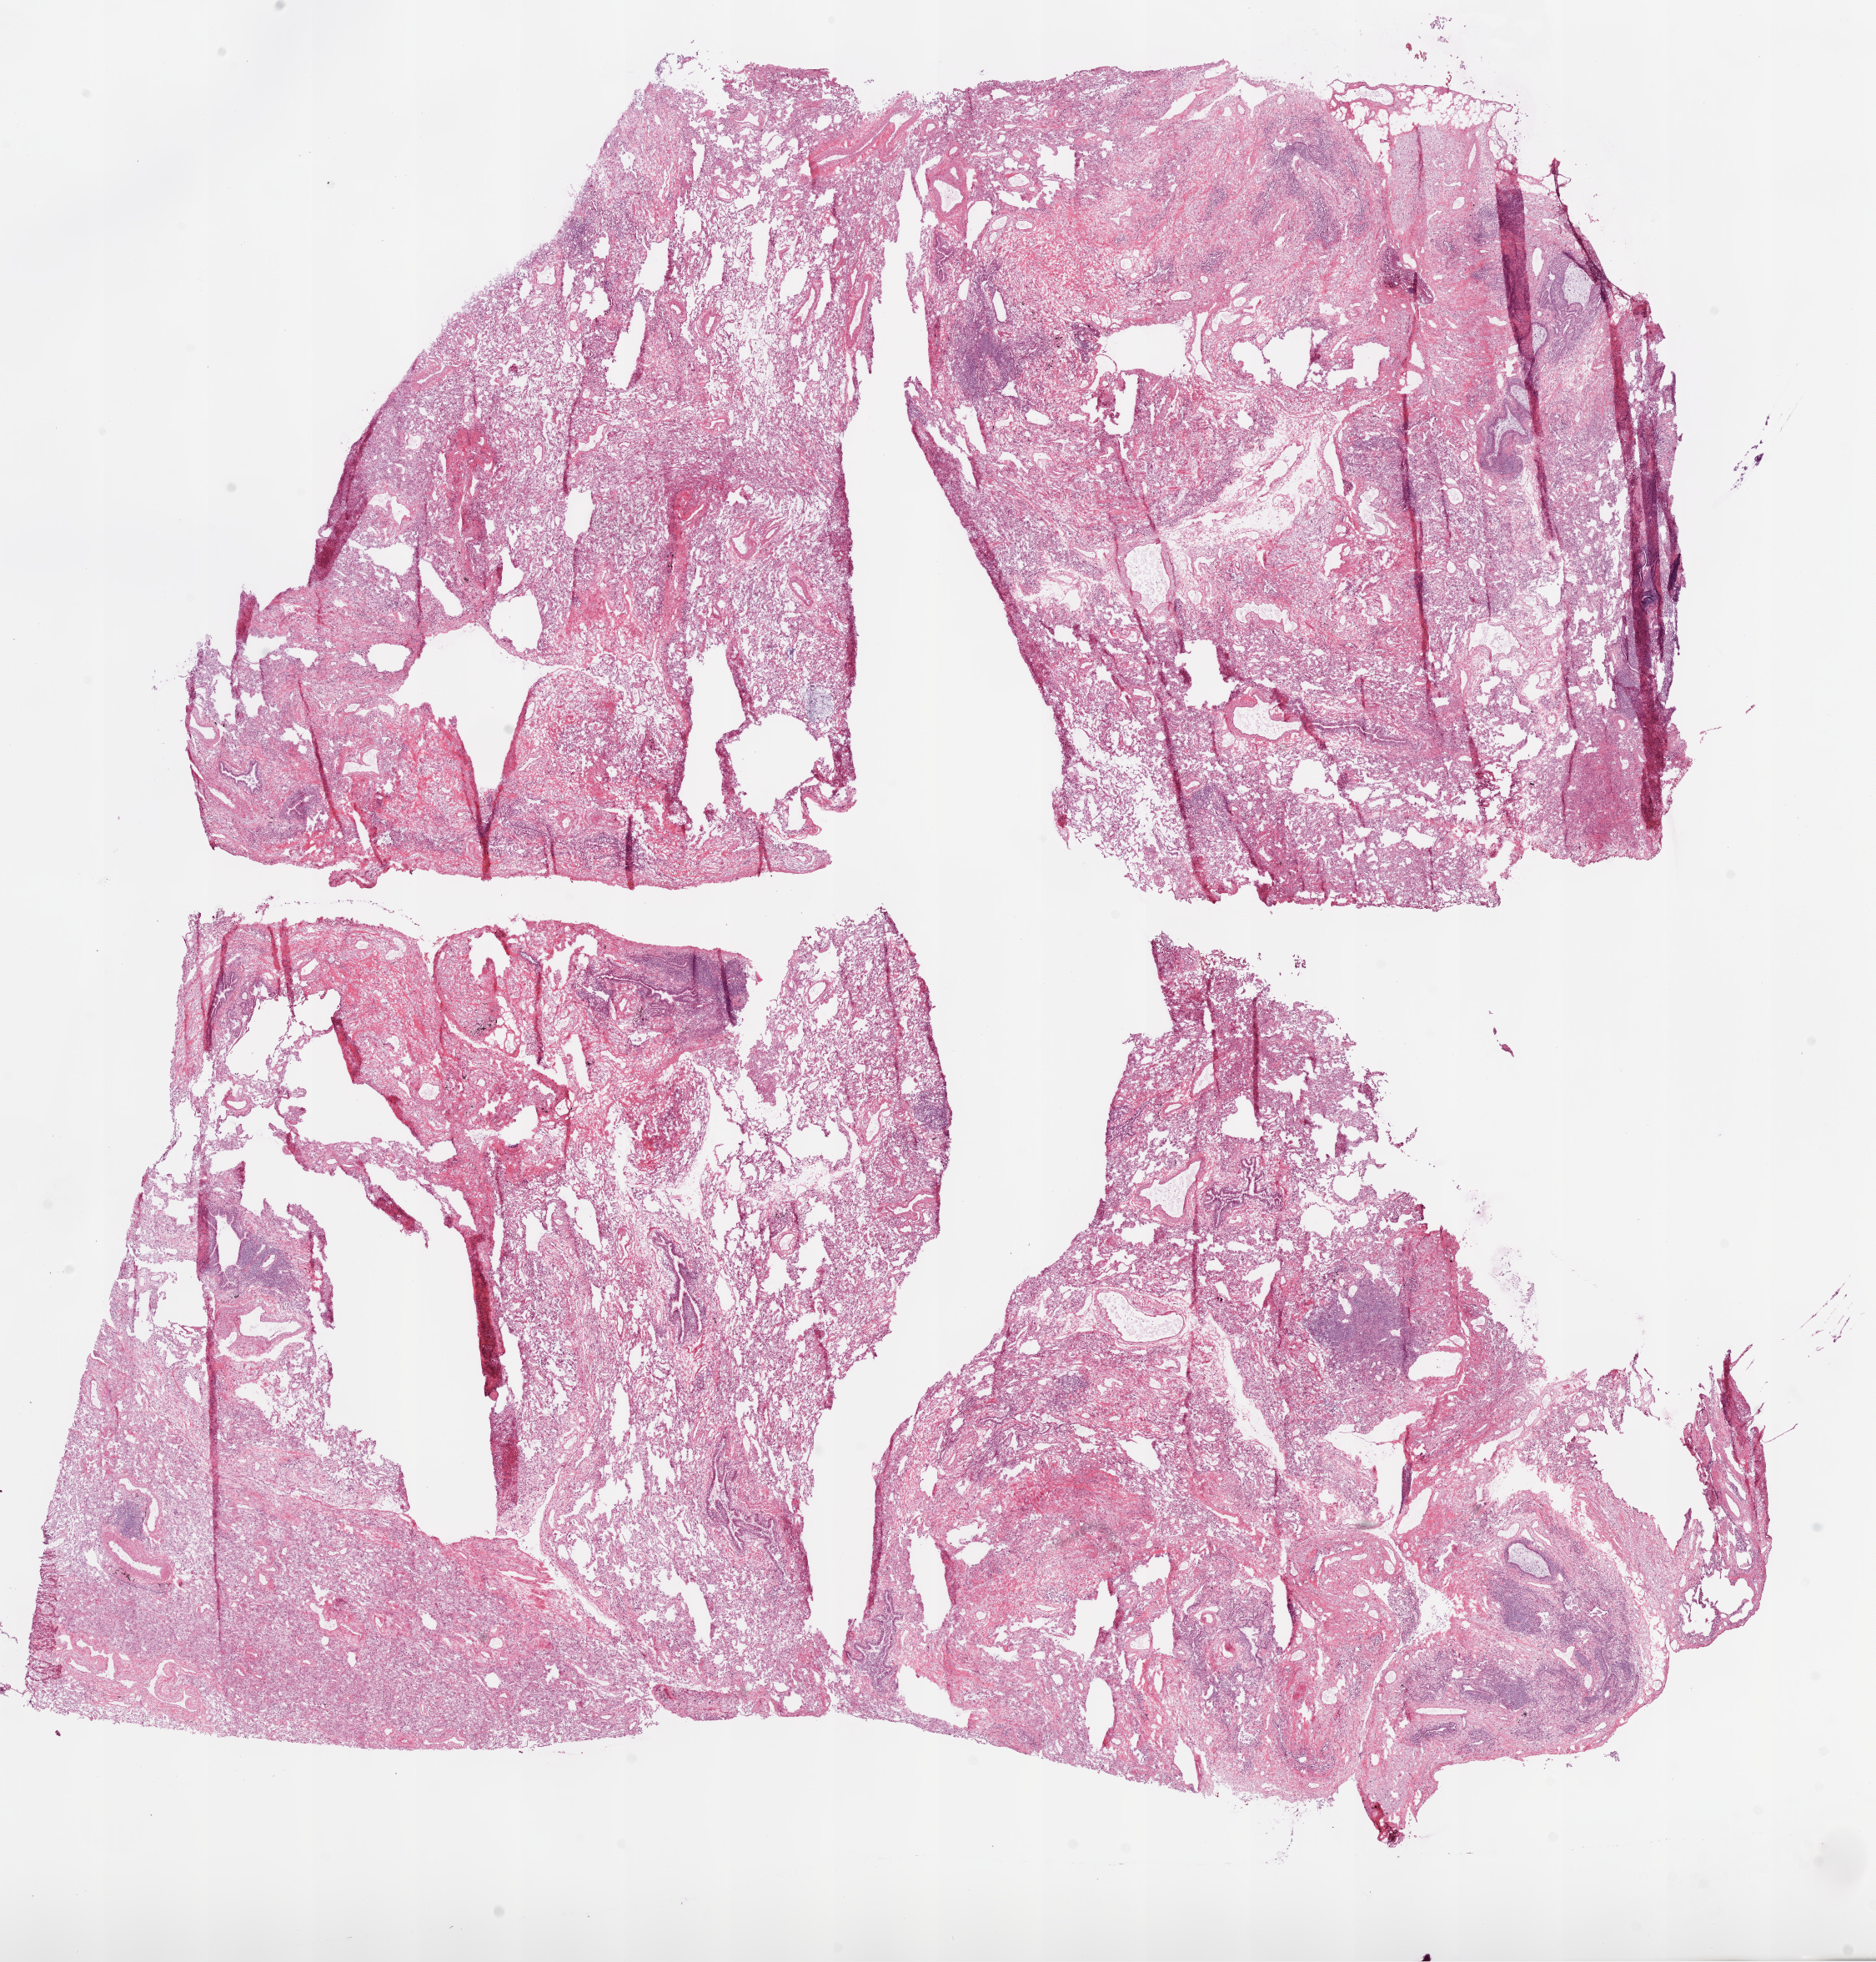
Whole-slide histology image, H&E-stained, low-resolution overview of the scanned area, about 18.1 x 18.9 mm; frozen section from the top of the tissue portion; sample: solid tissue normal (non-tumour tissue), lung. Female, age 81 years at initial diagnosis.
This section: solid tissue normal (non-tumour) sample from the same patient. Patient diagnosis: Squamous cell carcinoma, NOS (lower lobe, lung).